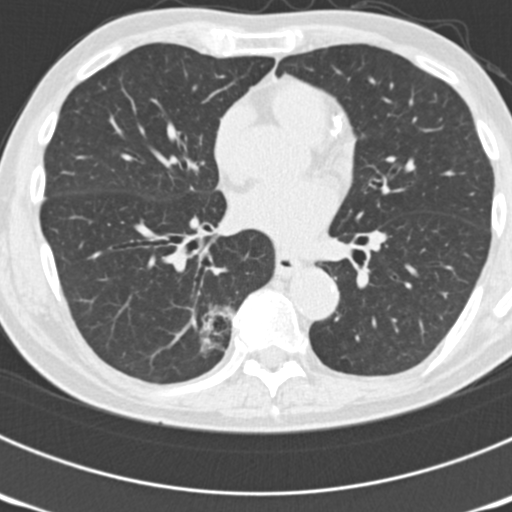
Chest CT (low-dose screening protocol), one axial image; third annual screen; lung window (W 1500 / L -600 HU); 2 mm slice thickness; standard (soft-tissue) reconstruction kernel (B30f); 120 kVp; slice 87 of 177 in the series; 512 × 512 image matrix. Male, age 70 years at enrolment.
- Lesion marked by an expert reader, box from (x=149, y=300) to (x=239, y=384) px.
- The screening reader recorded 3 non-calcified nodules or masses ≥4 mm on this exam (right upper lobe, left upper lobe, right lower lobe); which of them this box marks is not recorded.
- Lung cancer was diagnosed 14 days after this screen: bronchiolo-alveolar adenocarcinoma, NOS, right lower lobe, poorly differentiated (G3), stage IB (AJCC 6th edition), 30 mm at pathology.